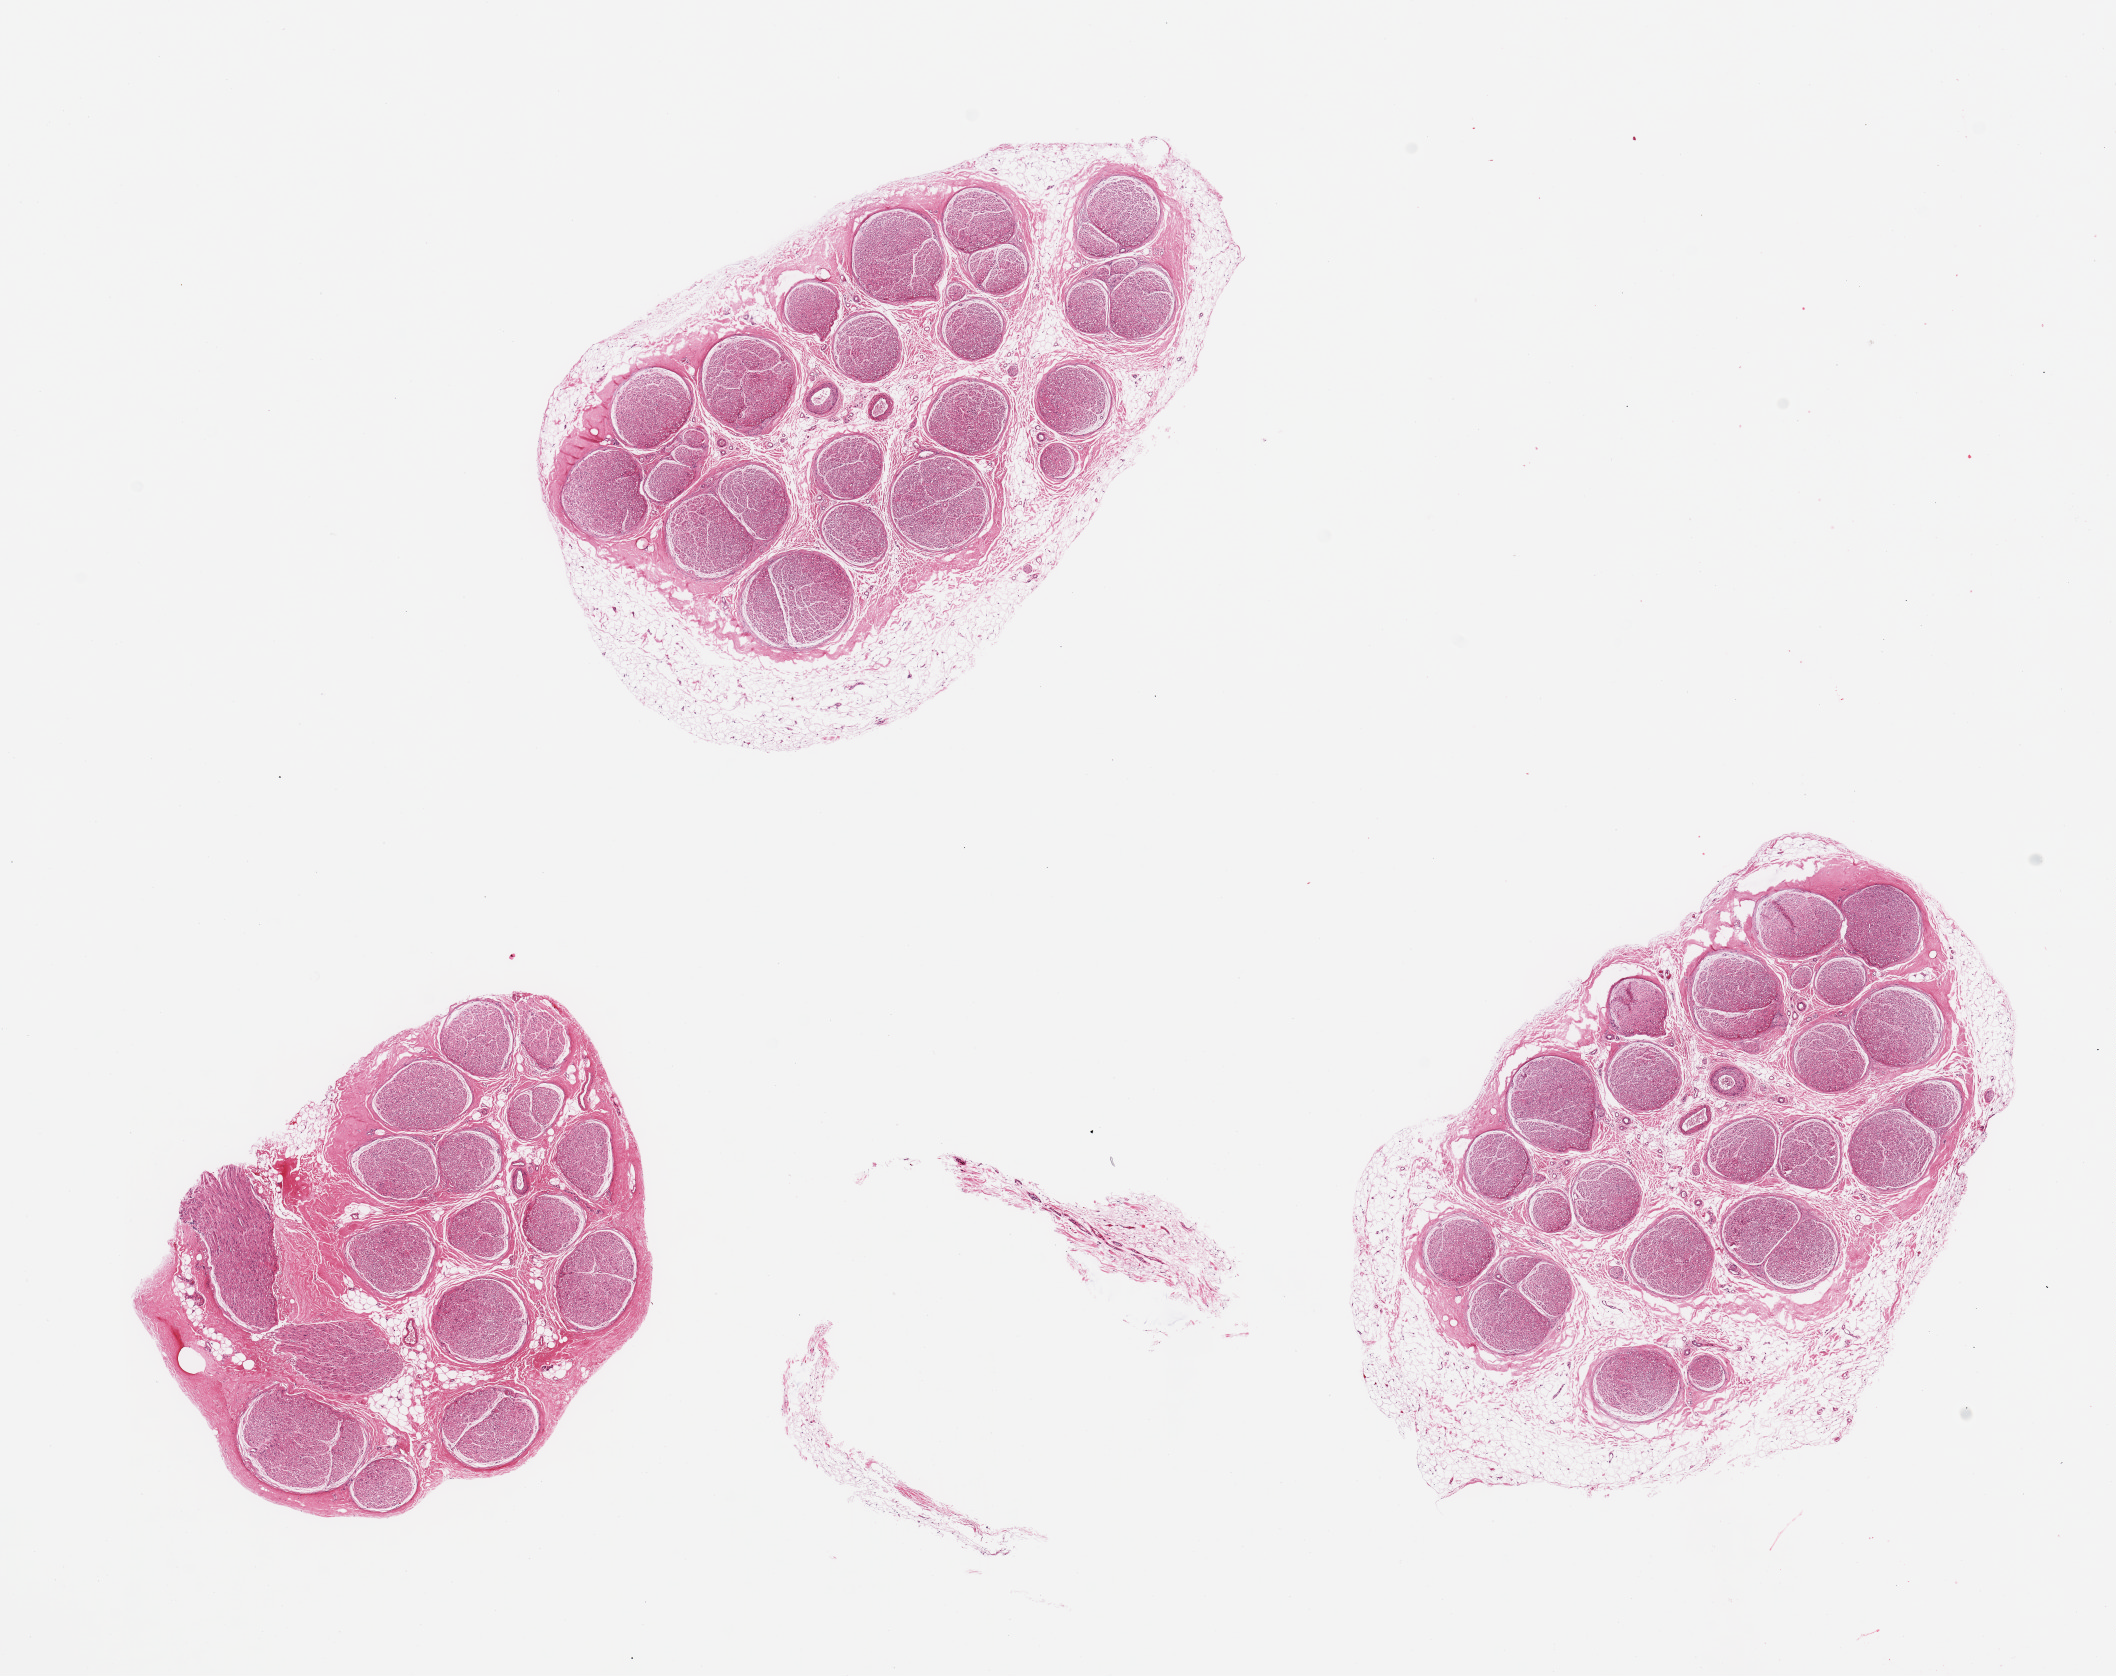
Whole-slide image, haematoxylin and eosin stain — low-resolution overview of the scanned area, about 16.7 x 13.3 mm. PAXgene-fixed paraffin-embedded (PFPE) section. Target tissue: tibial nerve. Tissue donor sample. Donor: female.
Reviewer comment on this tissue sample: 3 pieces; up to 20% internal fat.